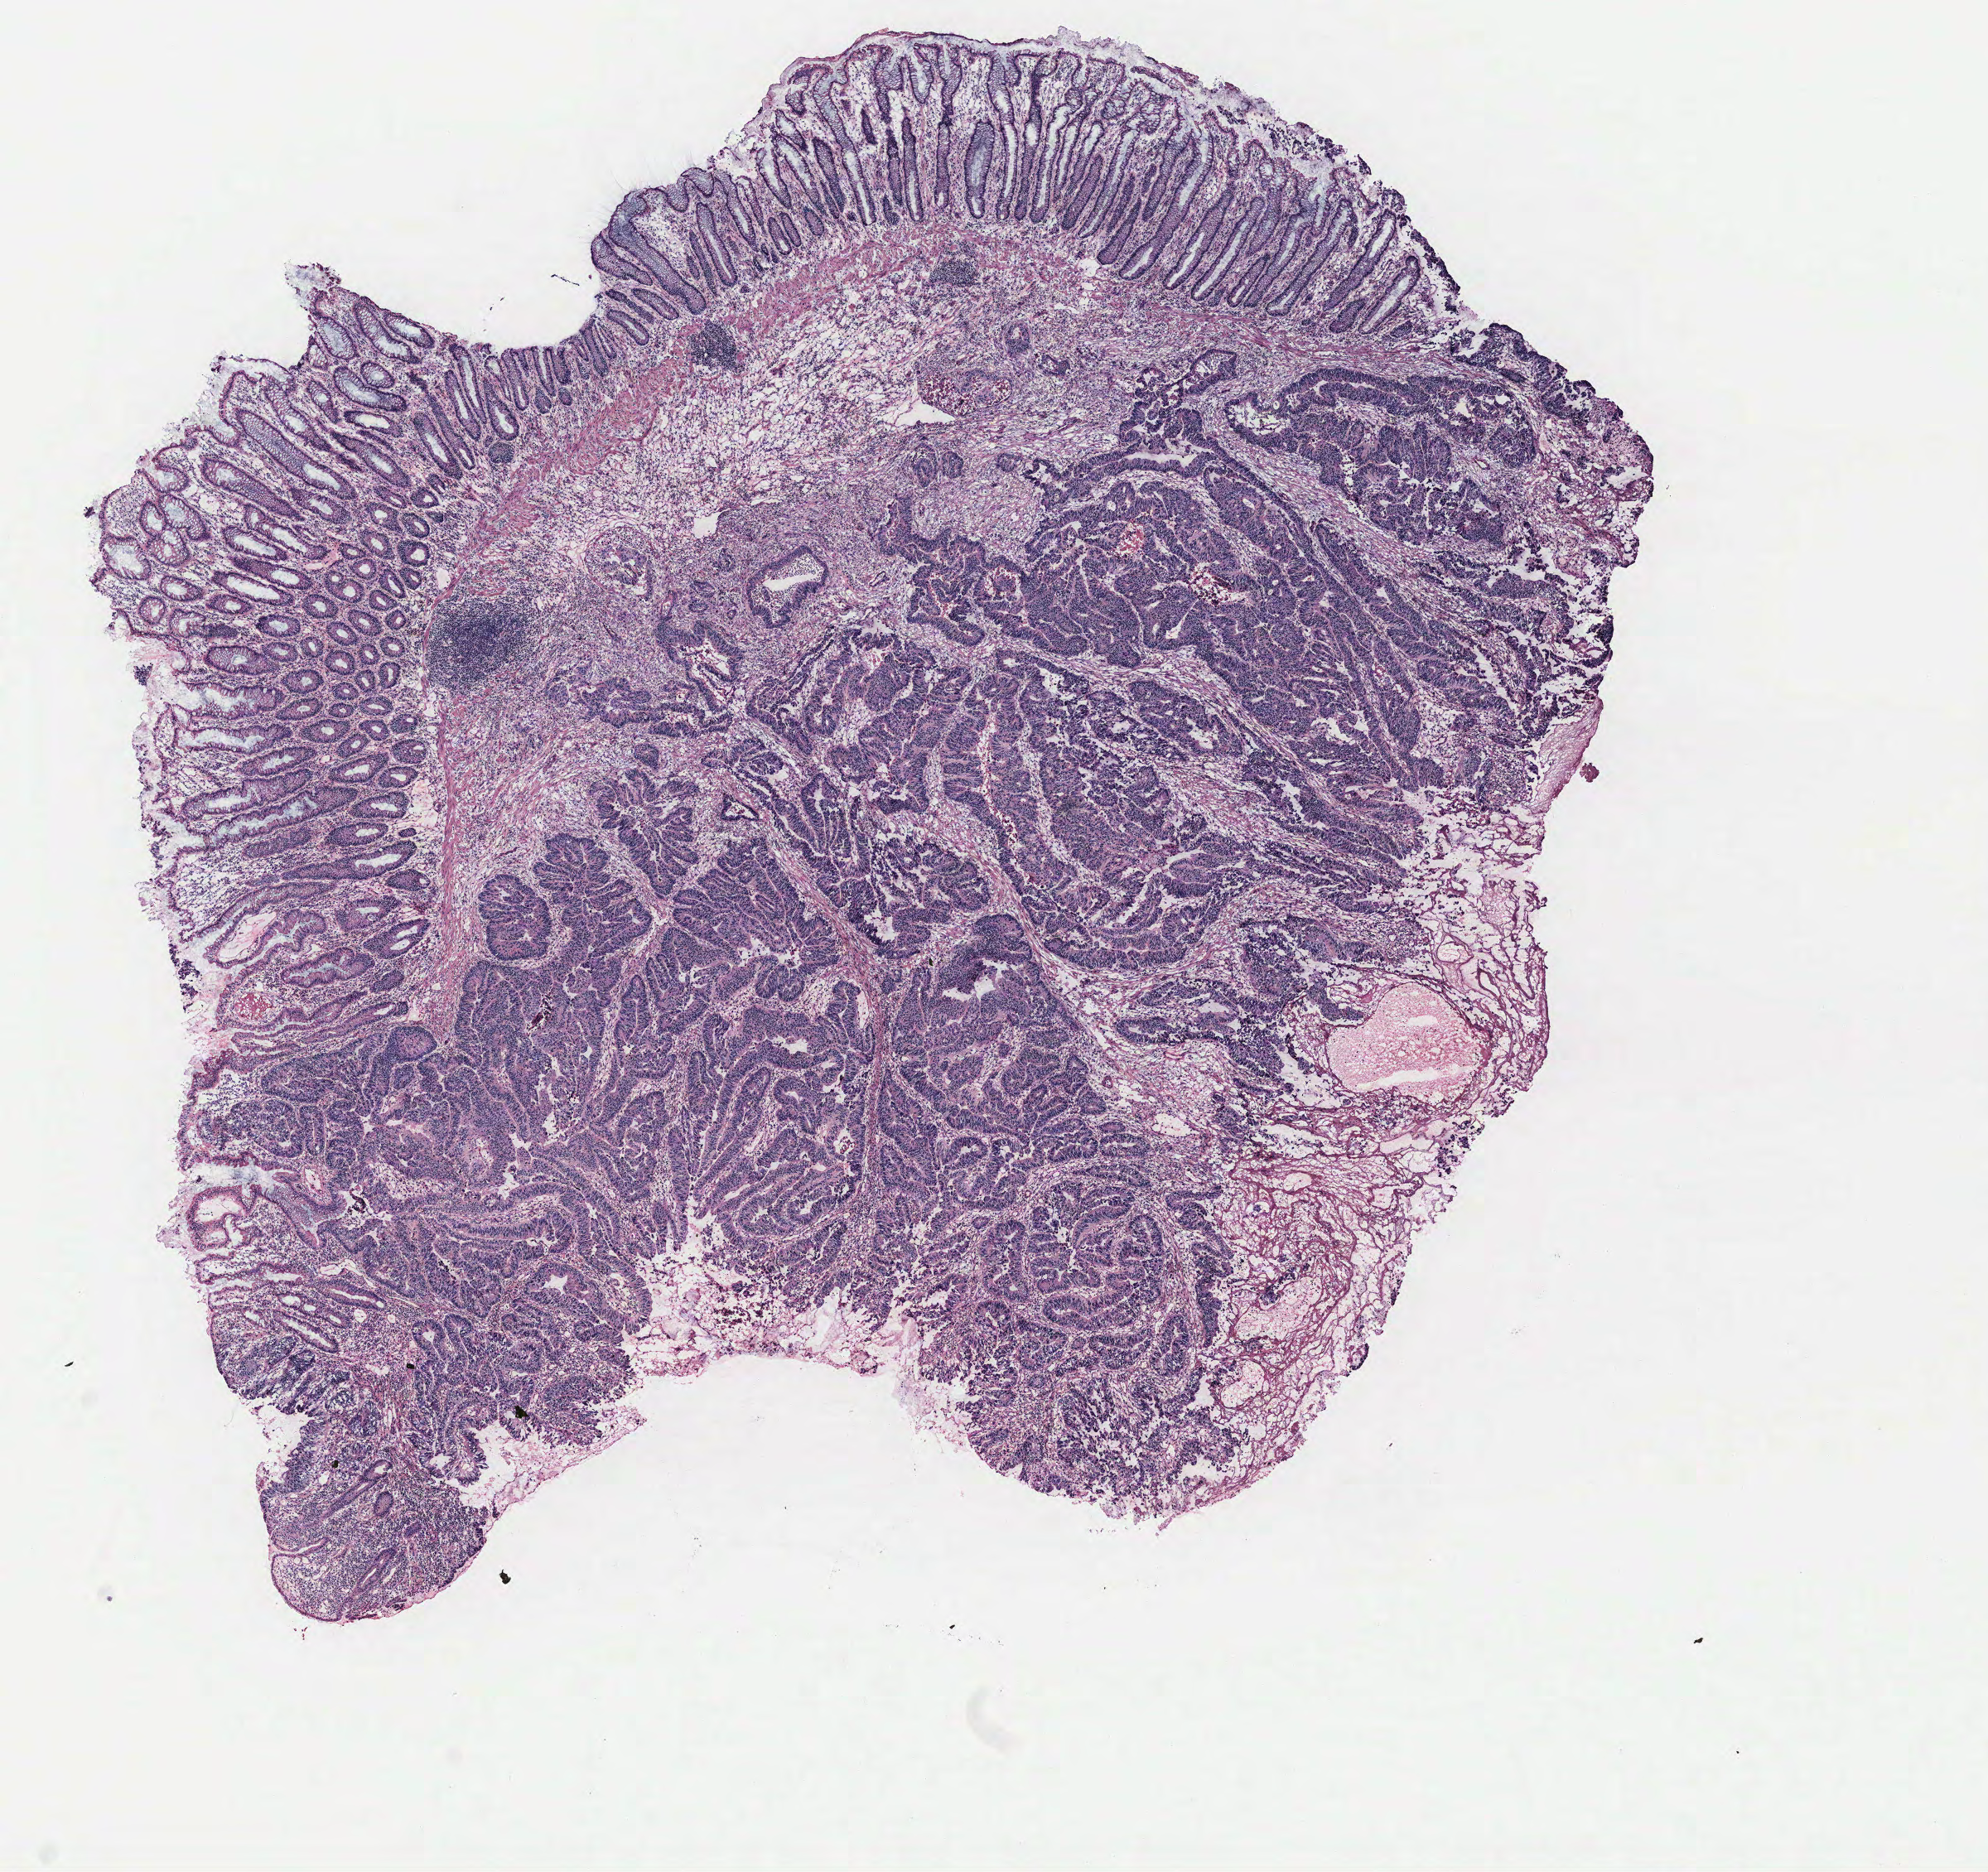
Hematoxylin and eosin (H&E) stained whole-slide image, whole scanned area (about 9.6 x 9.0 mm) shown as a low-resolution overview. Colon, tissue type not recorded. Male patient.
Patient diagnosis: Adenocarcinoma, NOS.